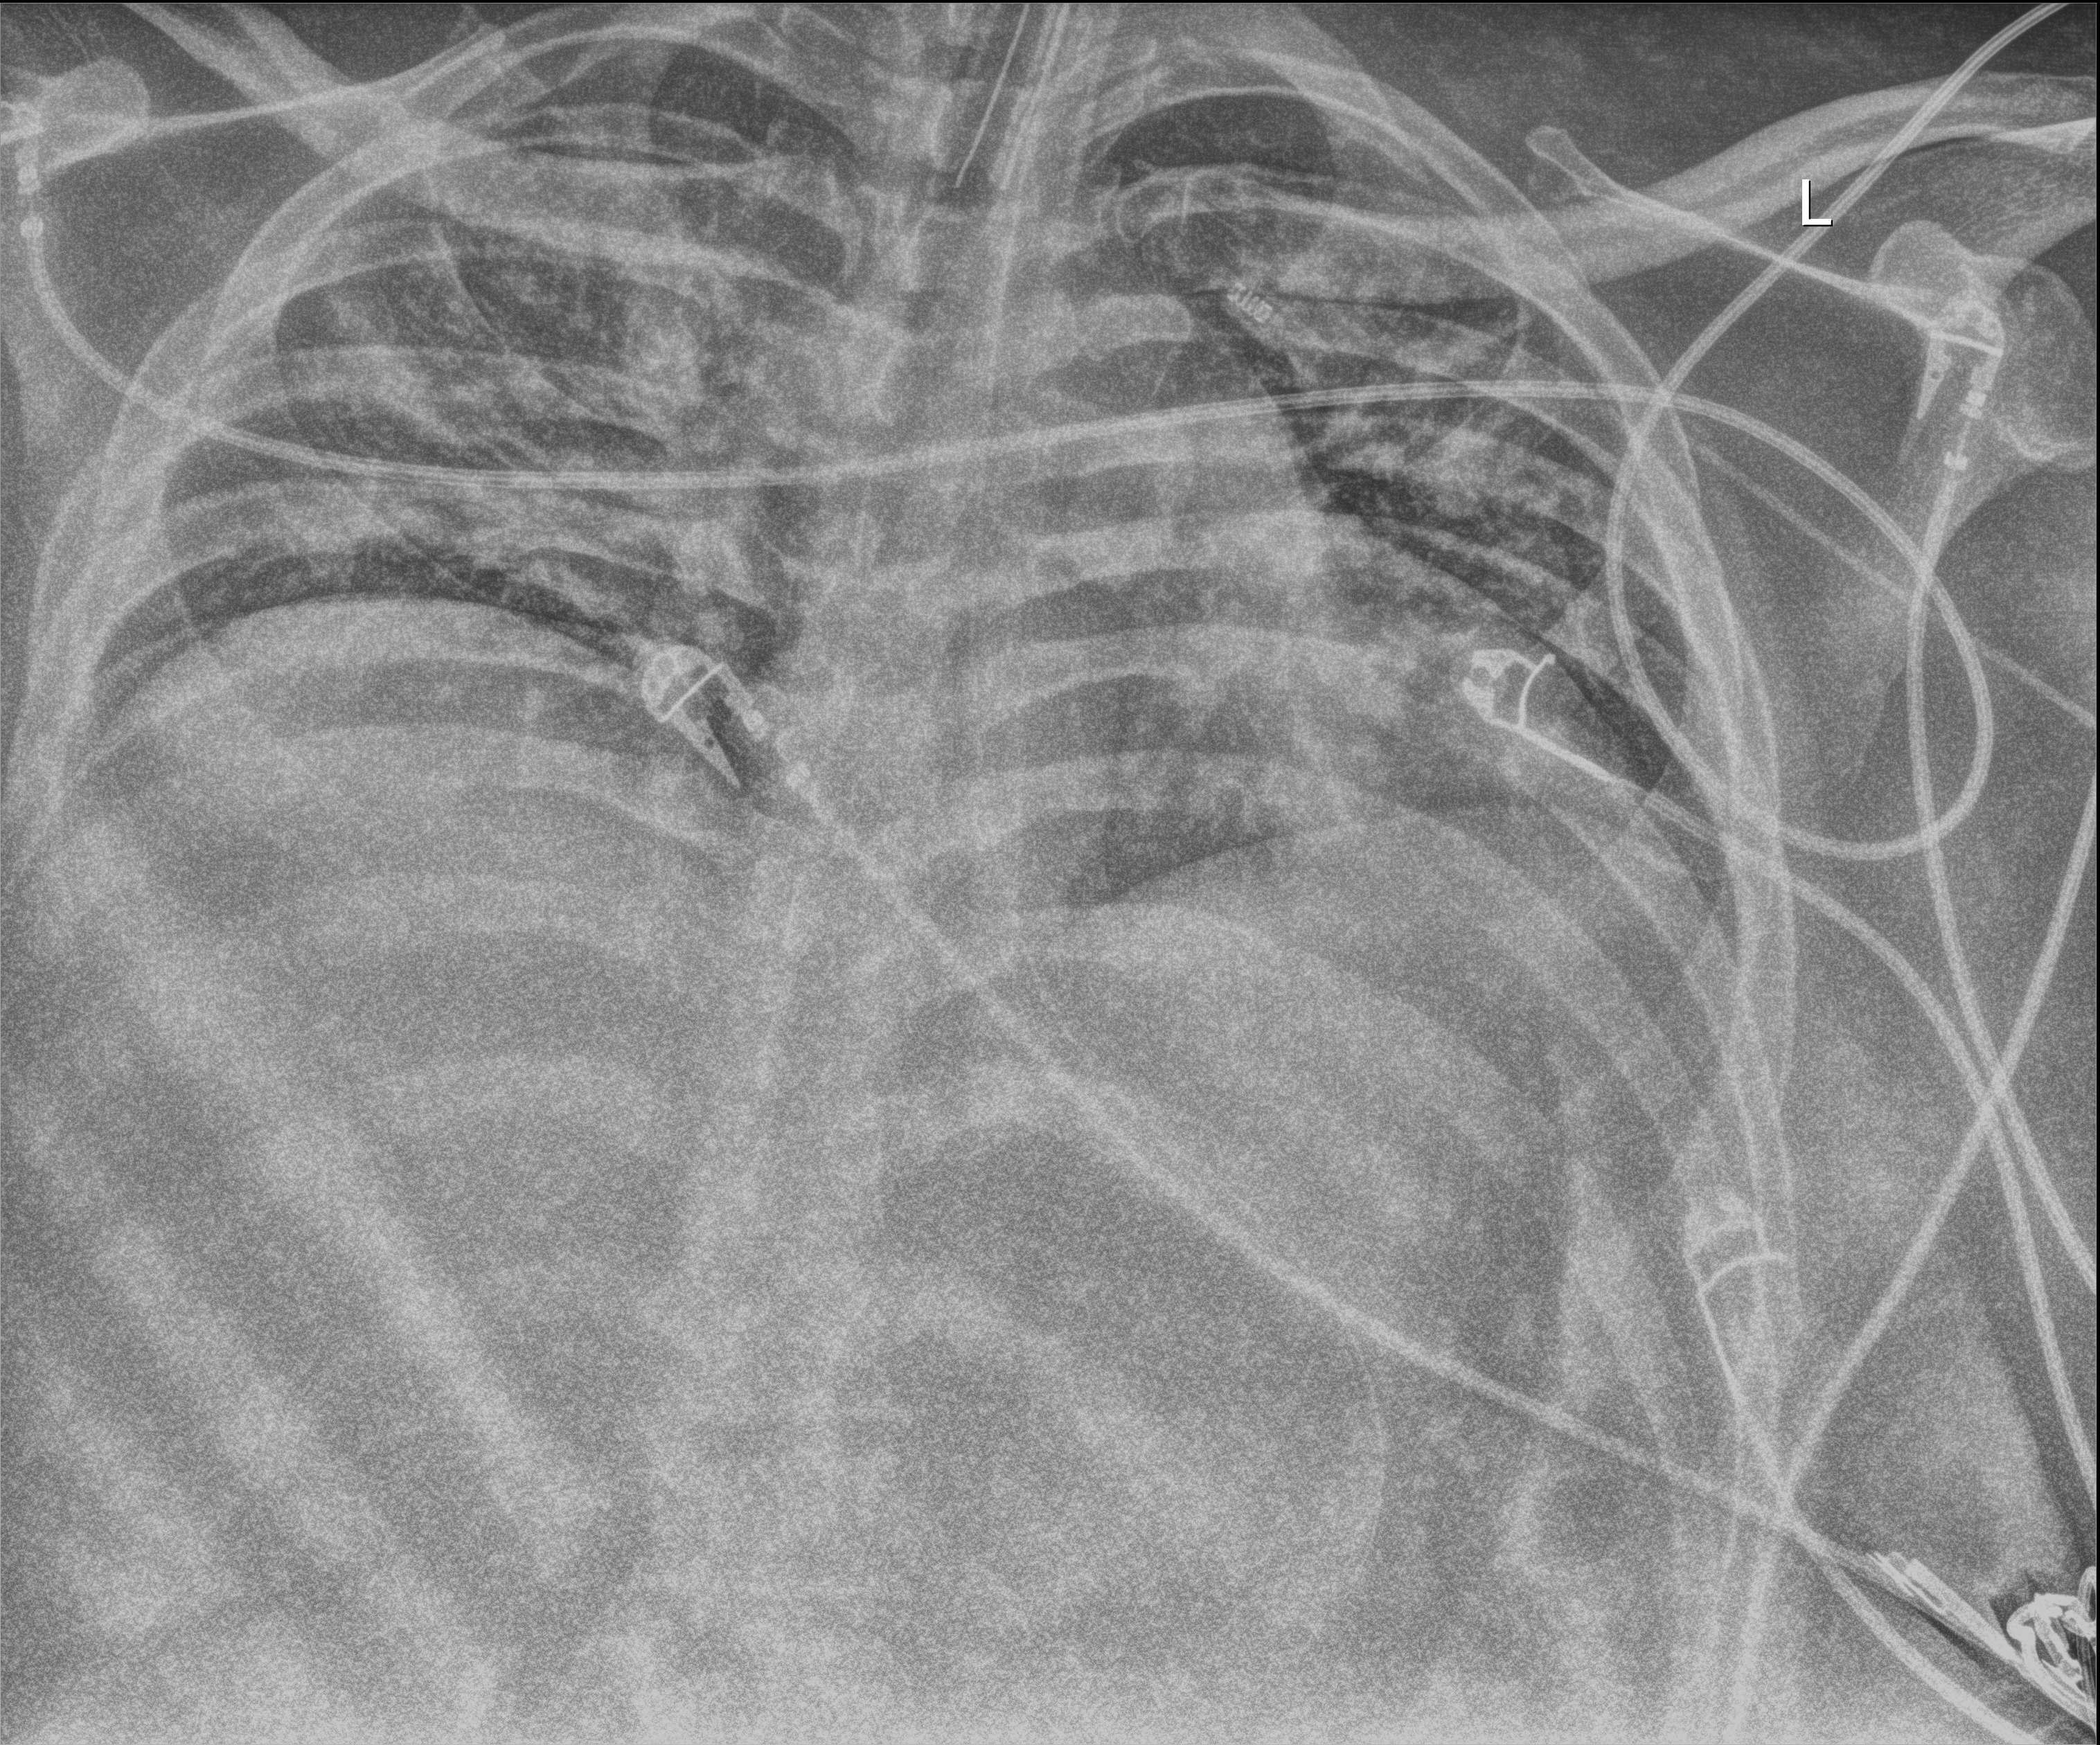
Portable chest radiograph, anteroposterior (AP) projection. Patient hospitalised with COVID-19; male, aged 18–59 years.
From the hospital-stay record, not from the radiograph (when in the stay this image was taken is not recorded):
- mechanically ventilated during this hospital stay: yes